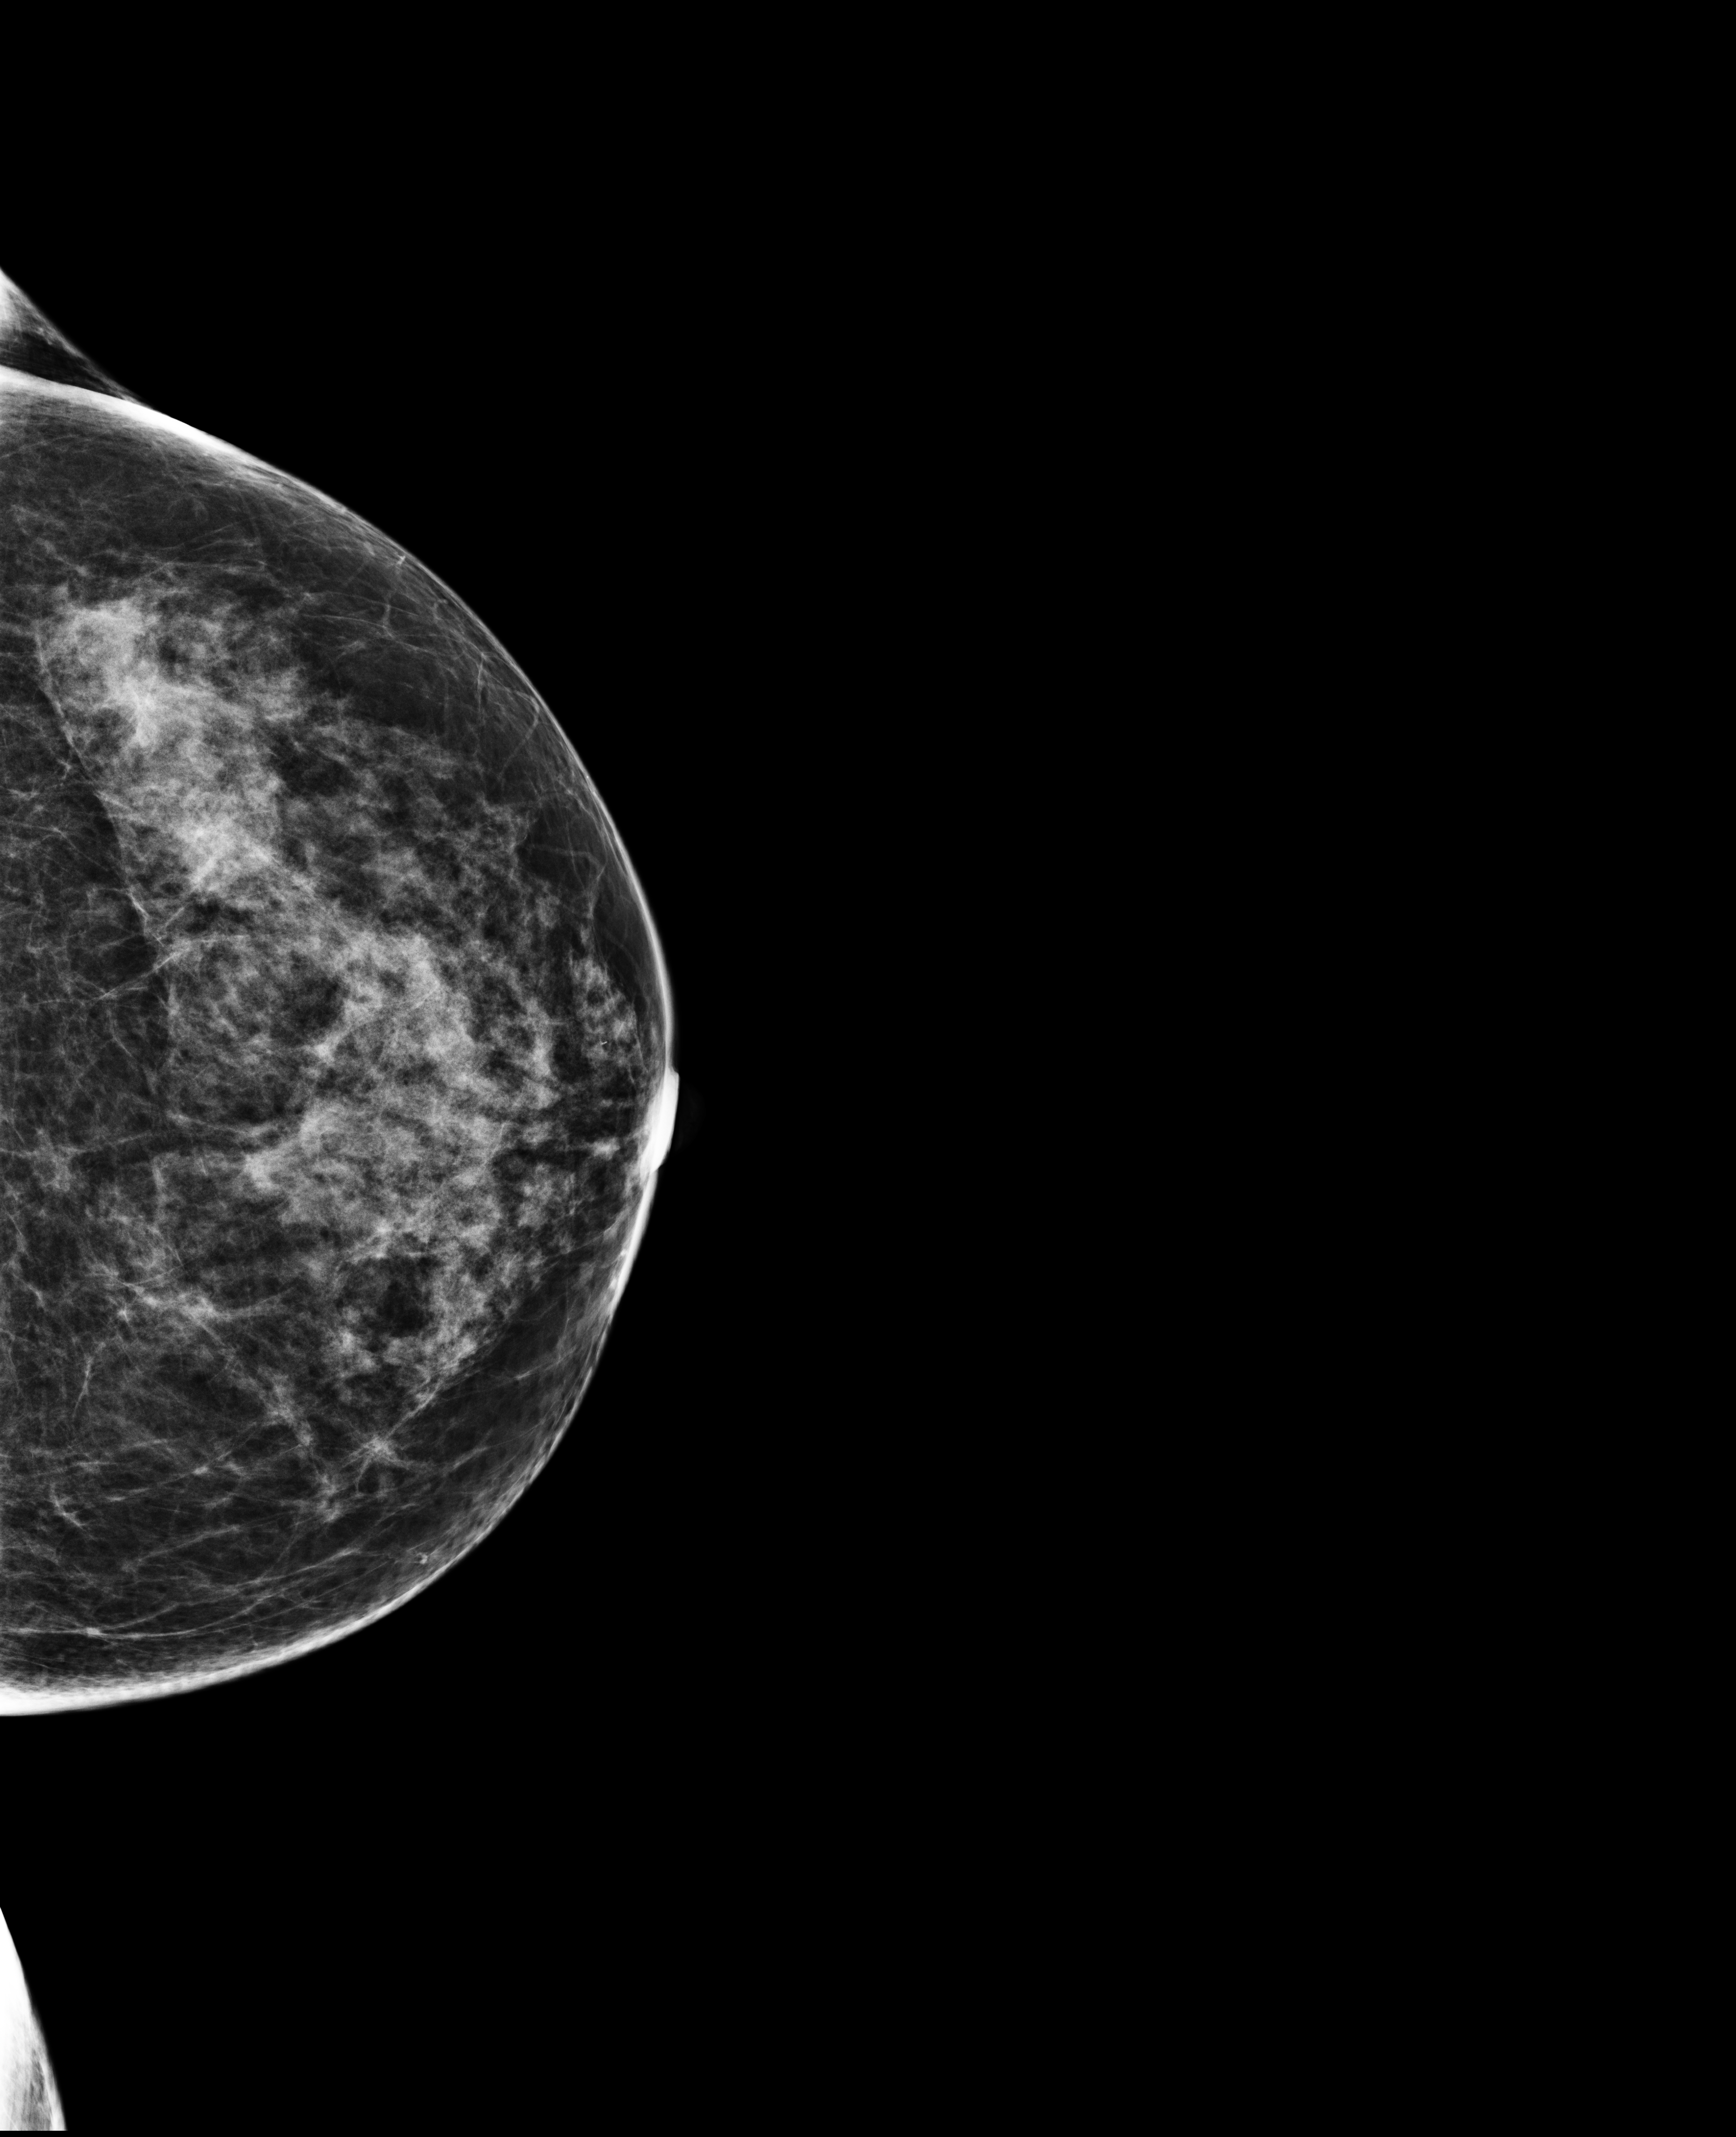
Screening examination, system: Selenia Dimensions.
Image type: full-field digital mammogram. Breast: left. Projection: CC view.